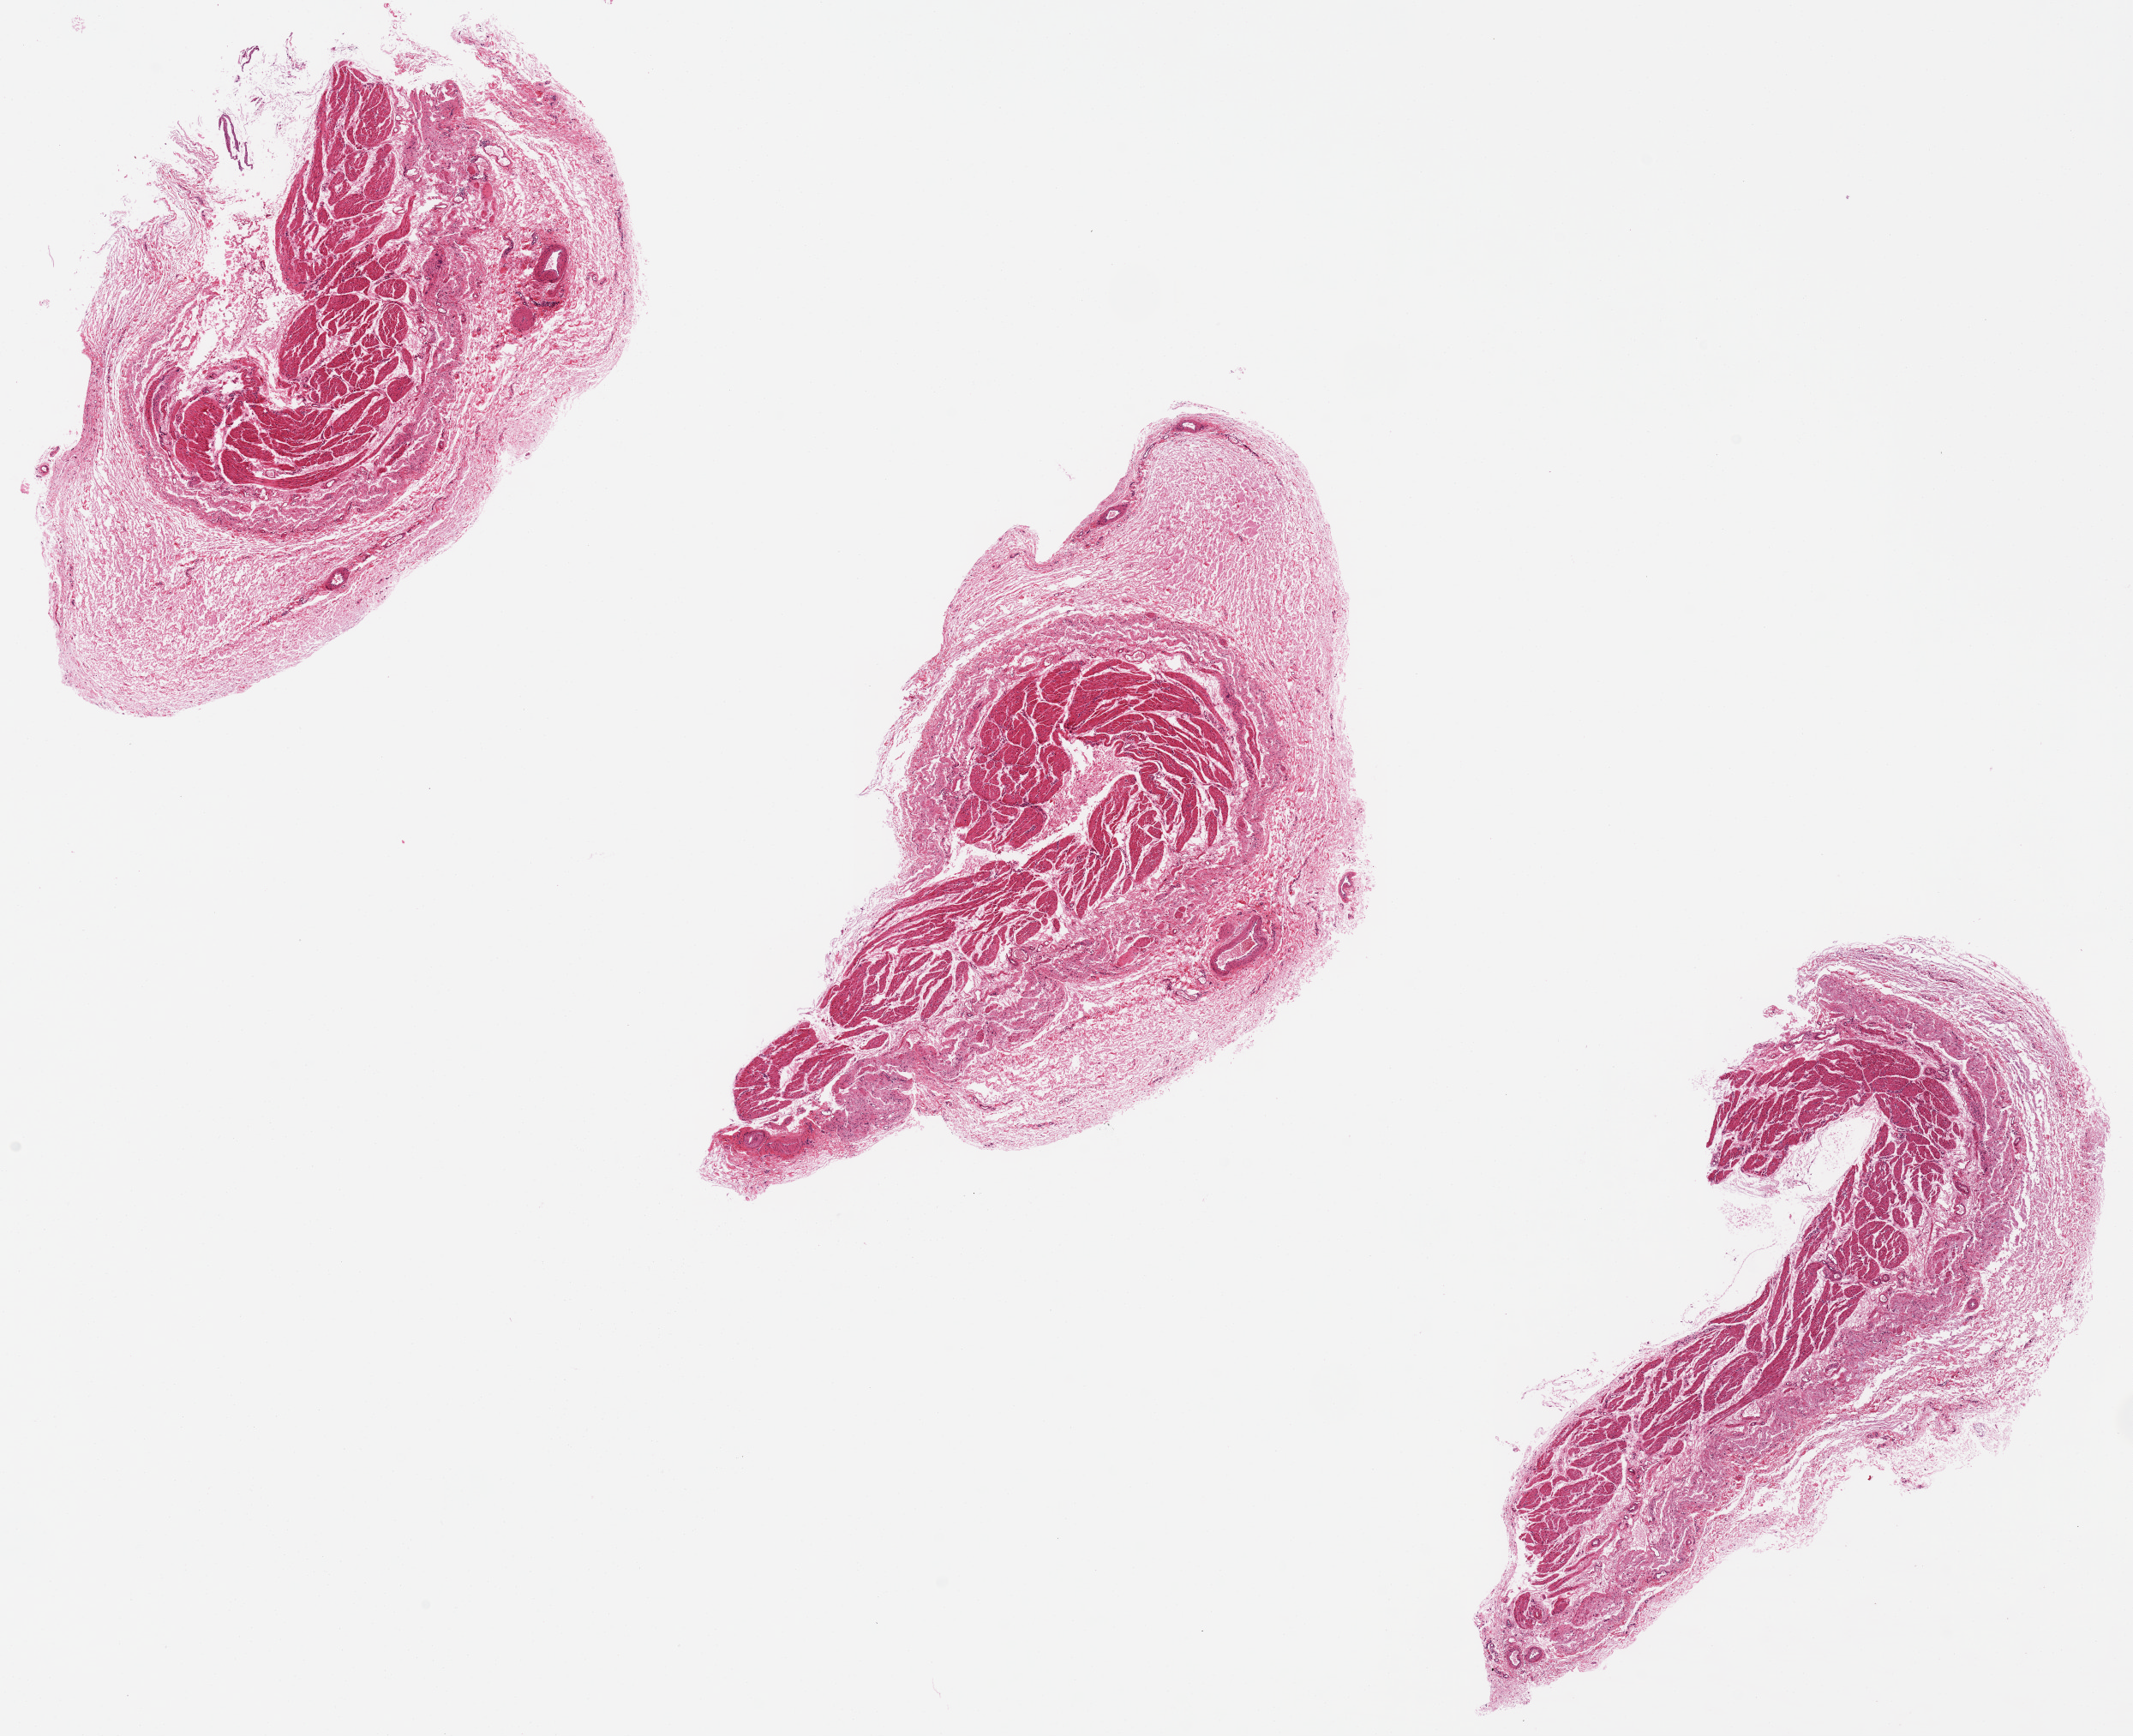
Digitized H&E-stained section — a low-resolution overview of the entire scanned area, about 19.7 x 16.0 mm. PAXgene-fixed, paraffin-embedded tissue. Section of esophageal mucous membrane (target tissue). Tissue donor sample. Donor sex: female.
Review note (as recorded): Good epithelium.